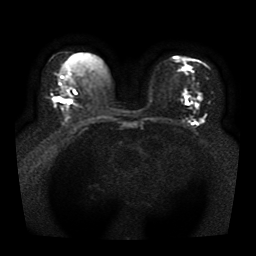
Breast MRI, one axial slice; position 20 of 41 along the scan axis; diffusion-weighted series; image 2 of 4 stored at this slice position (different b-values; order by instance number); 1.5 T; 256 × 256 image matrix. Female patient.
Annotated regions visible in this slice (outlined manually by an expert reader):
- tumour on diffusion-weighted imaging: box from (x=187, y=67) to (x=200, y=108) px